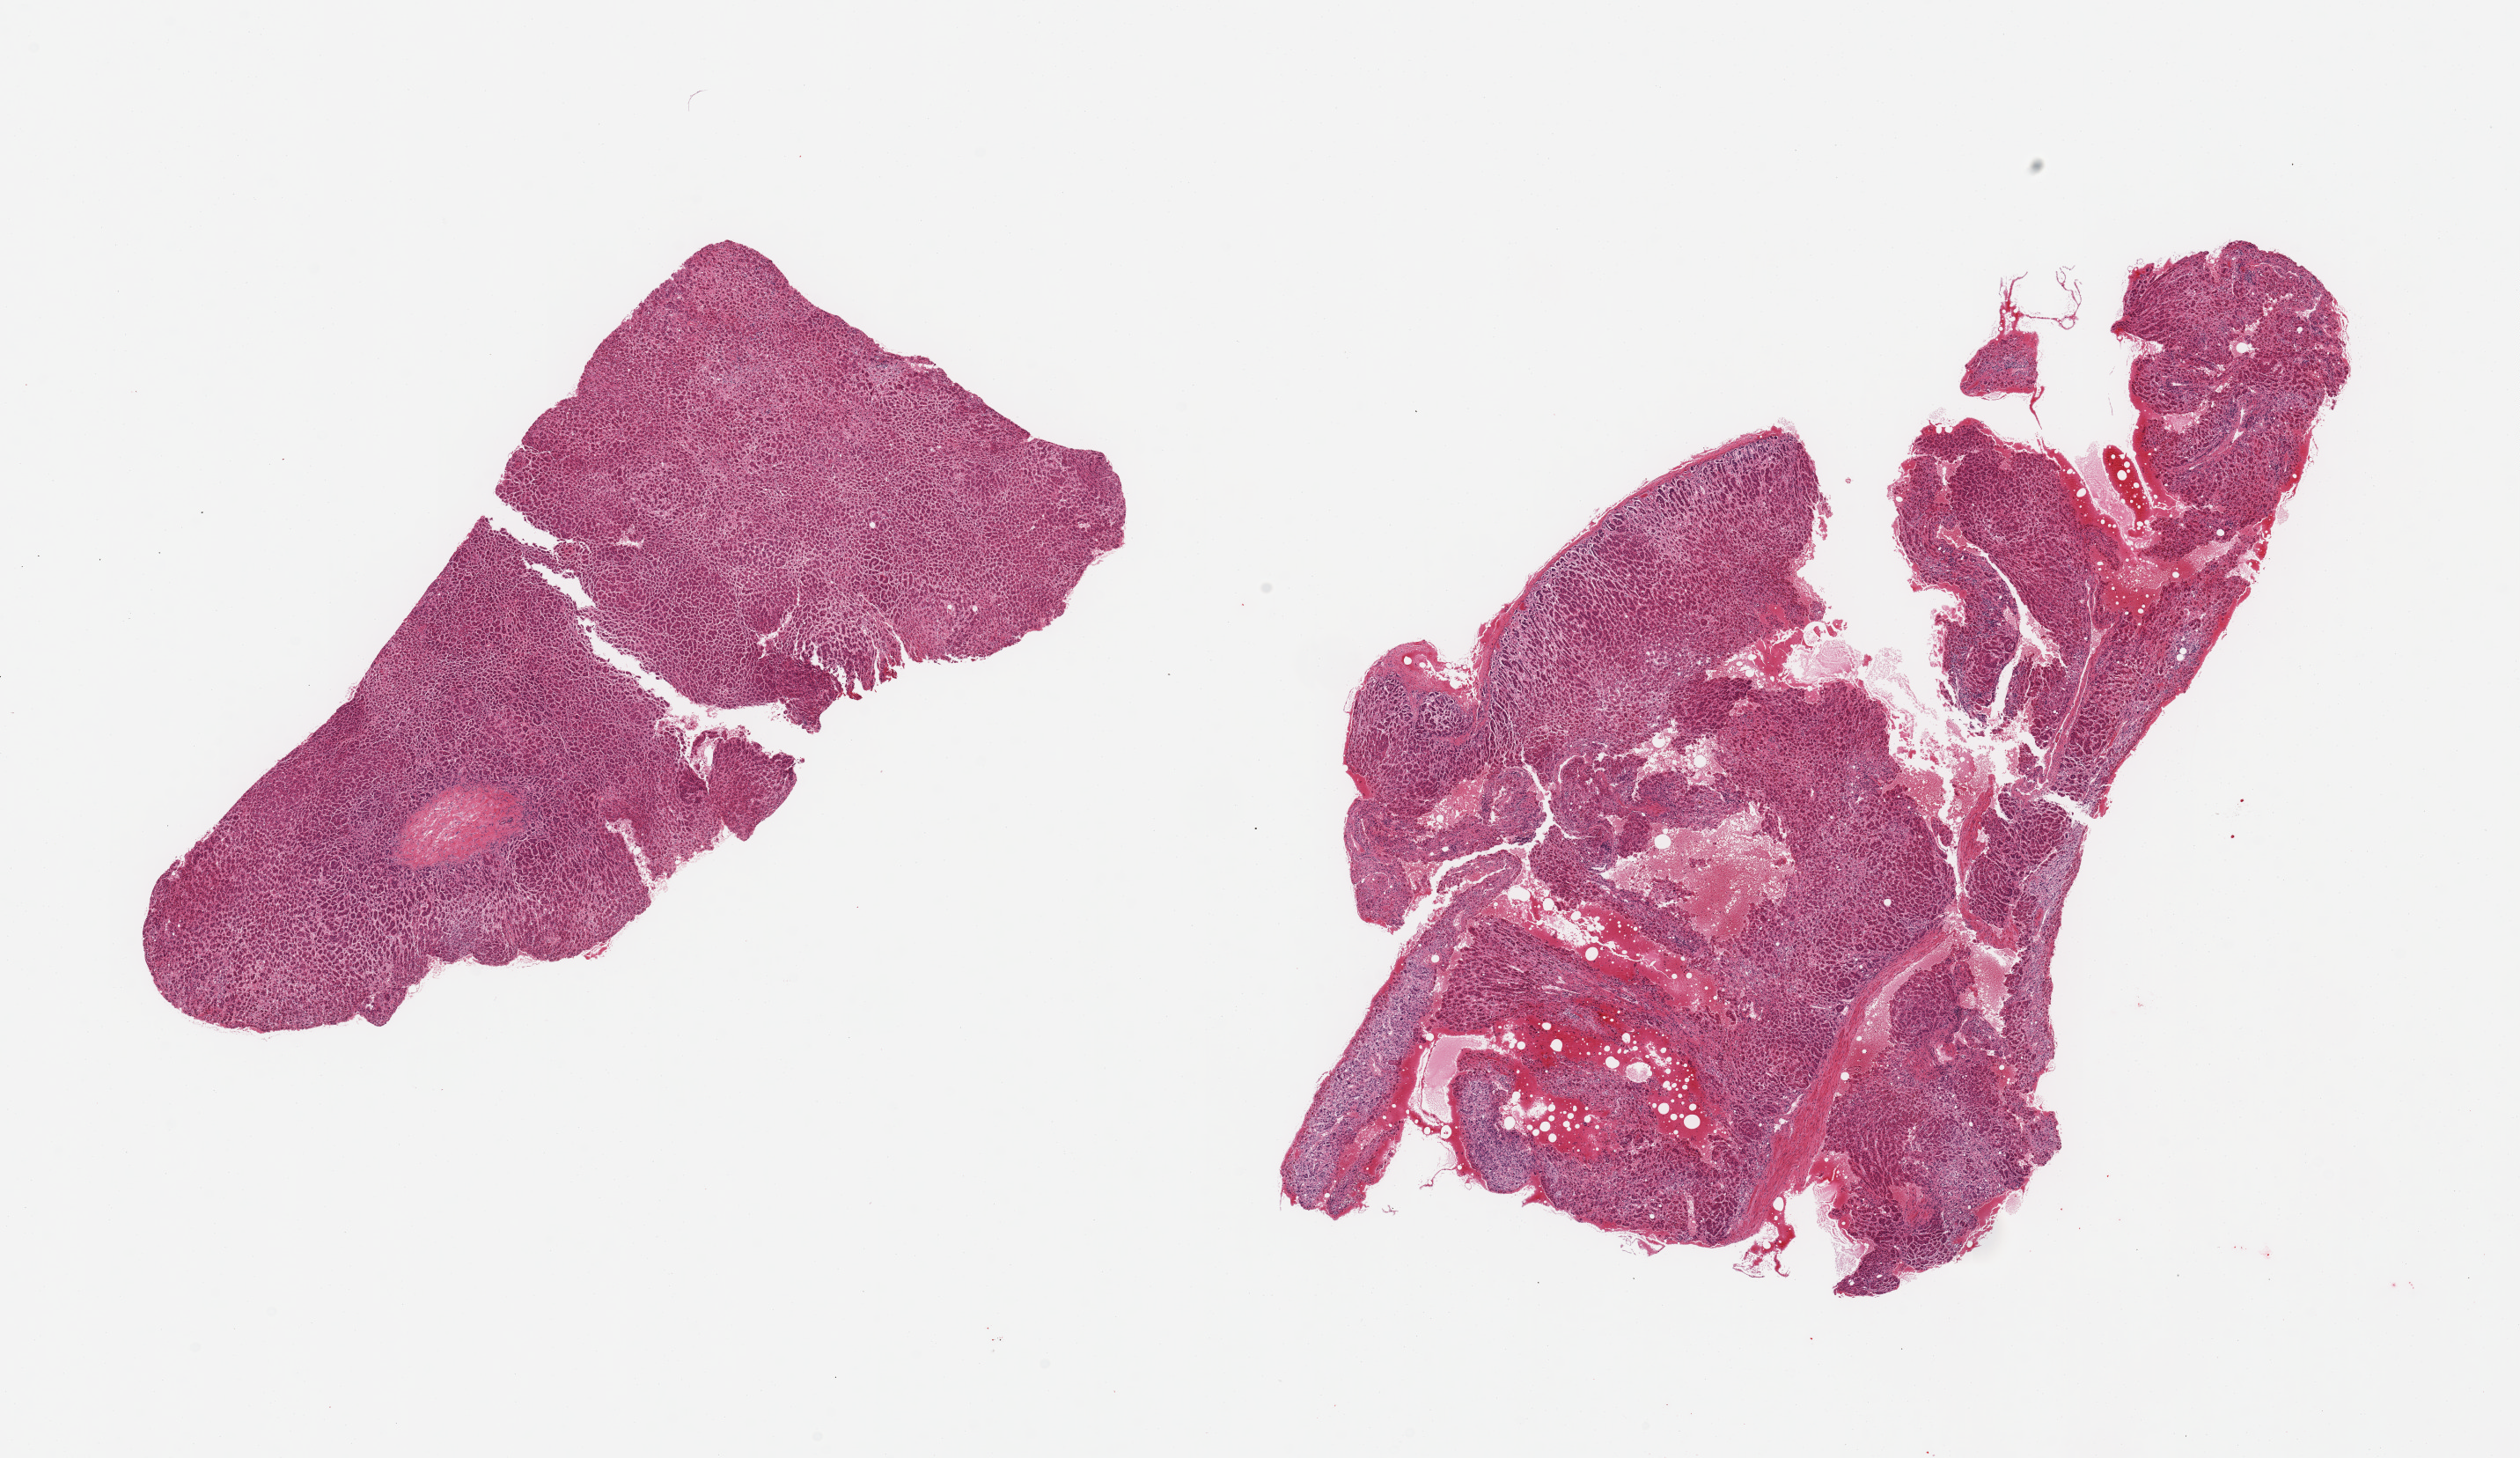
Haematoxylin and eosin whole-slide image — shown as a low-resolution overview of the whole scanned area (about 22.6 x 13.1 mm); PAXgene-fixed paraffin-embedded (PFPE) section; sampled site (target tissue): adrenal gland; tissue donor sample. Donor sex: male.
• reviewer comment on this tissue sample: 2 pieces, cortex, advanced autolysis